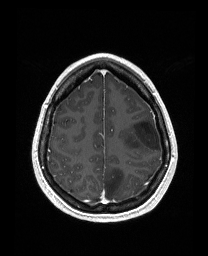
Brain MRI from a brain-tumour surgery series, one axial slice. Slice 124 of 176 in the series (ordered by position). T1-weighted post-contrast. 1 mm slice thickness. 208 × 256 image matrix, field of view 203 × 250 mm. From the clinical record (not read from this slice): histopathology: Astrocytoma; WHO grade: 3; IDH mutation: yes; tumour location: Left Frontal.
Annotated regions visible in this slice (manually delineated by an expert):
- tumour: bounding box (x1, y1, x2, y2) in pixels: (123, 117, 161, 151)